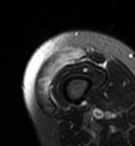
MRI of an extremity soft-tissue mass, one axial slice; slice 6 of 95 in the series (ordered by position); T2-weighted fat-saturated; MR volume resampled by the dataset authors to the PET/CT grid (not the native acquisition matrix); 3.27 mm slice thickness; 135 × 146 image matrix, field of view 132 × 143 mm. Female patient. From the clinical record (not read from this slice): histological type: pleiomorphic undifferentiated sarcoma; grade: high; site of the primary tumour: right quadricep.
Structures marked on this image (expert contour drawn on MRI and transferred to this co-registered scan by the dataset authors):
- gross tumour volume including surrounding oedema: bounding box <58,47,84,60> (left, top, right, bottom; pixels)